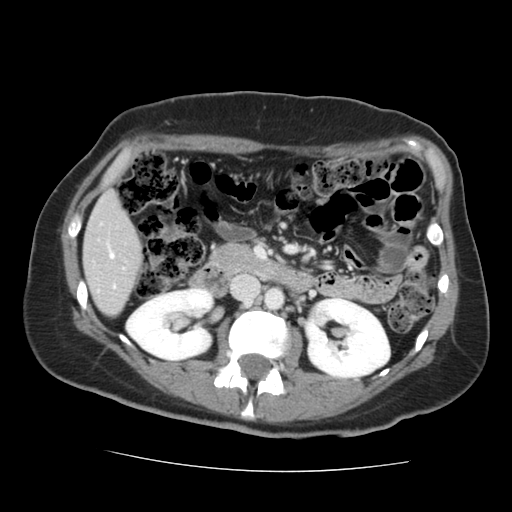
Contrast-enhanced abdominal CT, one axial slice; slice 60 of 144 in the series (ordered by position); 120 kVp; intravenous contrast given; soft-tissue window (W 400 / L 40 HU); 2.5 mm slice thickness; 512 × 512 image matrix. Female patient, age 46 years. From the clinical record (not read from this slice): diagnosis: colorectal cancer liver metastases, imaged before liver resection; multiple liver metastases: no; largest metastasis: 2.8 cm; disease in both lobes: no.
Outlined on this slice (outlined manually by an expert reader):
- liver: box from (x=84, y=194) to (x=140, y=315) px
- planned liver remnant (the part of the liver to remain after resection): (x=84, y=194)–(x=140, y=255)
- portal vein (with intrahepatic branches): (x=109, y=250)–(x=115, y=287)